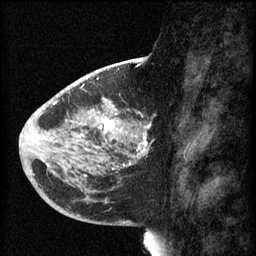
Breast MRI (dynamic contrast-enhanced), one sagittal slice; position 26 of 60 along the scan axis; 3 images stored at this slice position (order not interpretable as contrast timing); 1.5 T; TE 4.2 ms, TR 8.1 ms; 256 × 256 image matrix, field of view 200 × 200 mm. Female patient, age 44 years.
Outlined on this slice (semi-automatic segmentation, software-assisted and operator-edited):
- analysis volume of interest (the breast-tissue region the enhancement analysis was run in; not a lesion): bounding box <59,110,151,169> (left, top, right, bottom; pixels)
- tumour enhancement mask (voxels above the 70 % enhancement threshold inside the analysis volume of interest): <78,112,151,169>